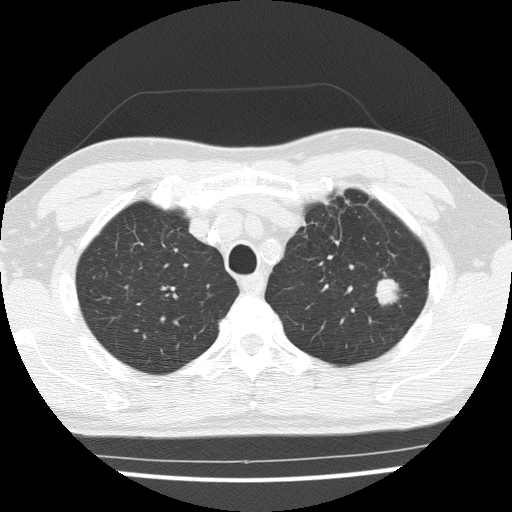
Low-dose screening chest CT, one axial slice. Position 119 of 154 along the scan axis. 120 kVp. Lung window (W 1500 / L -600 HU). 512 × 512 image matrix.
Outlined on this slice (outlined manually by an expert reader):
- lesion 1 (tumor, upper lobe of left lung): box from (x=376, y=273) to (x=398, y=305) px